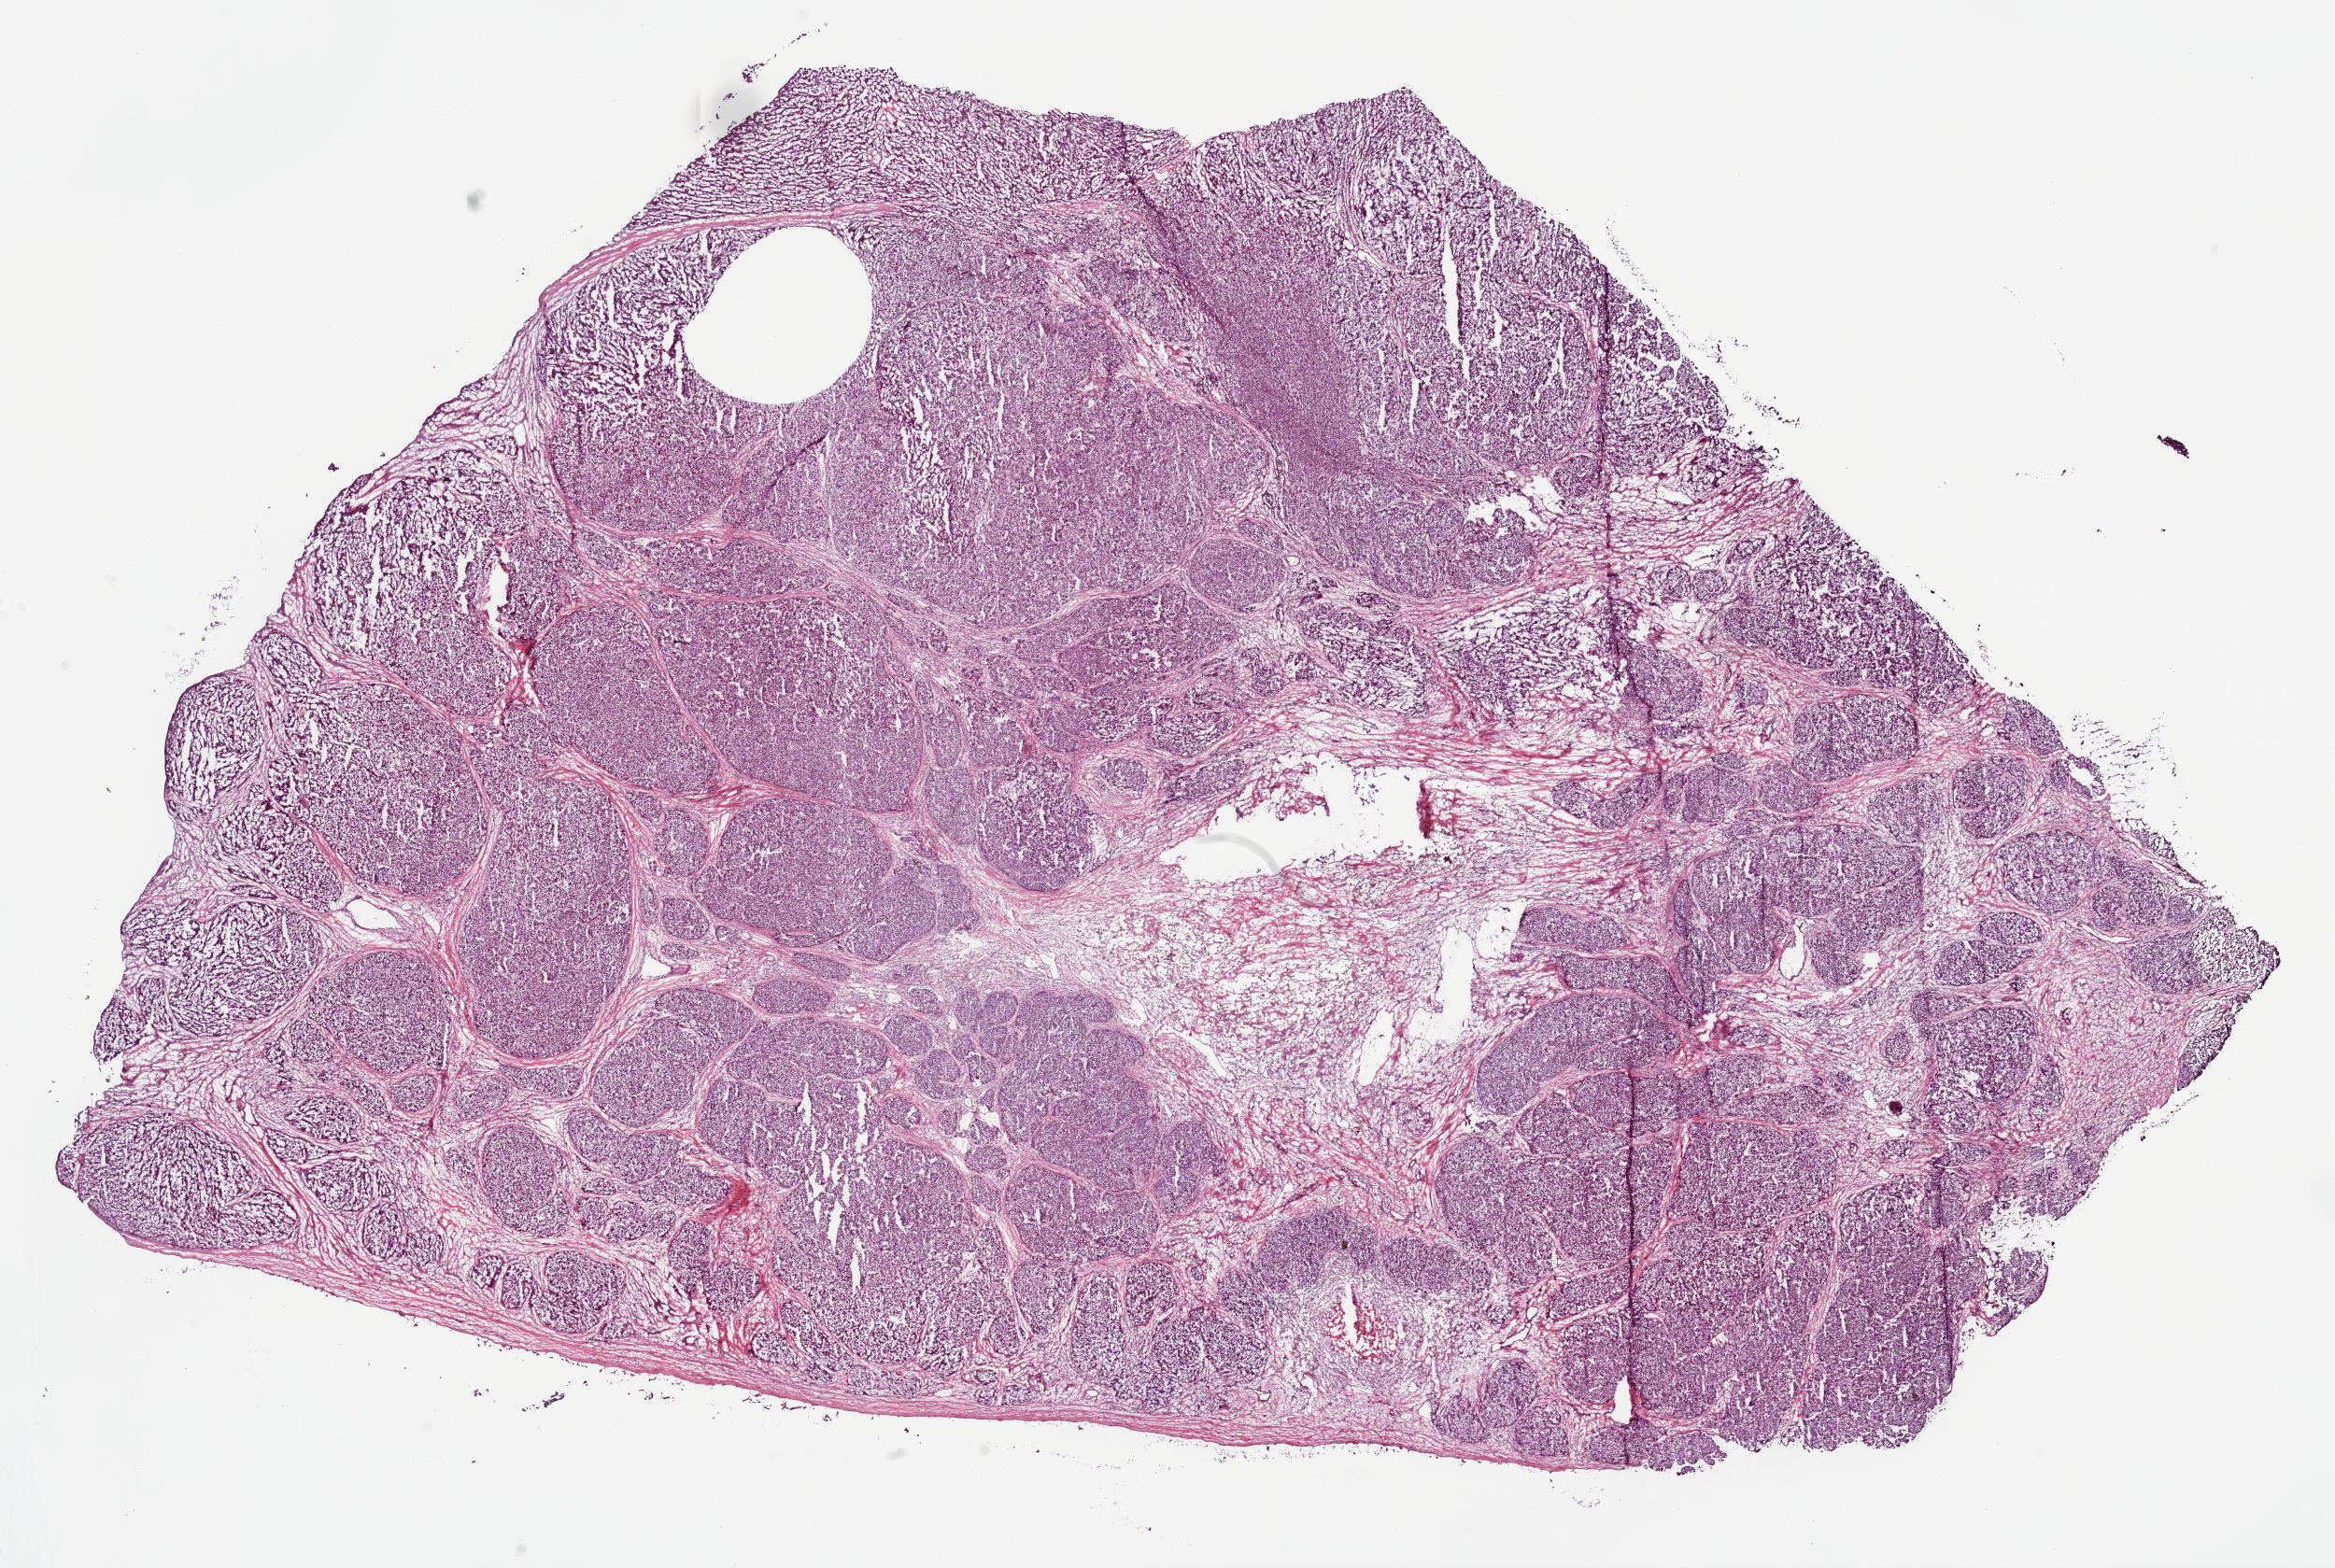
Whole-slide histology image, Hematoxylin and eosin (H&E) stained, a low-resolution overview of the entire scanned area, about 20.1 x 13.5 mm. Frozen section from the bottom of the tissue portion. Primary tumour sample from the liver. Patient: male, age at initial diagnosis 67 years. Histologic grade: G1 (well differentiated). Pathologist review of this section (percent, as recorded): tumour cells 80%, tumour nuclei 85%, normal cells 0%, stromal cells 20%, necrosis 0%.
• AJCC pathologic stage: IIIC (7th edition)
• diagnosis: Hepatocellular carcinoma, NOS